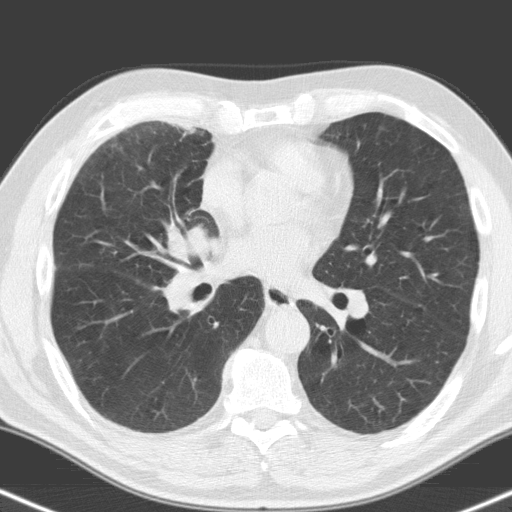
Low-dose screening chest CT, one axial slice. Slice 80 of 160 in the series (ordered by position). 120 kVp. Lung window (W 1500 / L -600 HU). 3.2 mm slice thickness. 512 × 512 image matrix.
Annotated regions visible in this slice (outlined manually by an expert reader):
- lesion 1 (tumor, hilum of right lung): bounding box <165,227,221,309> (left, top, right, bottom; pixels)